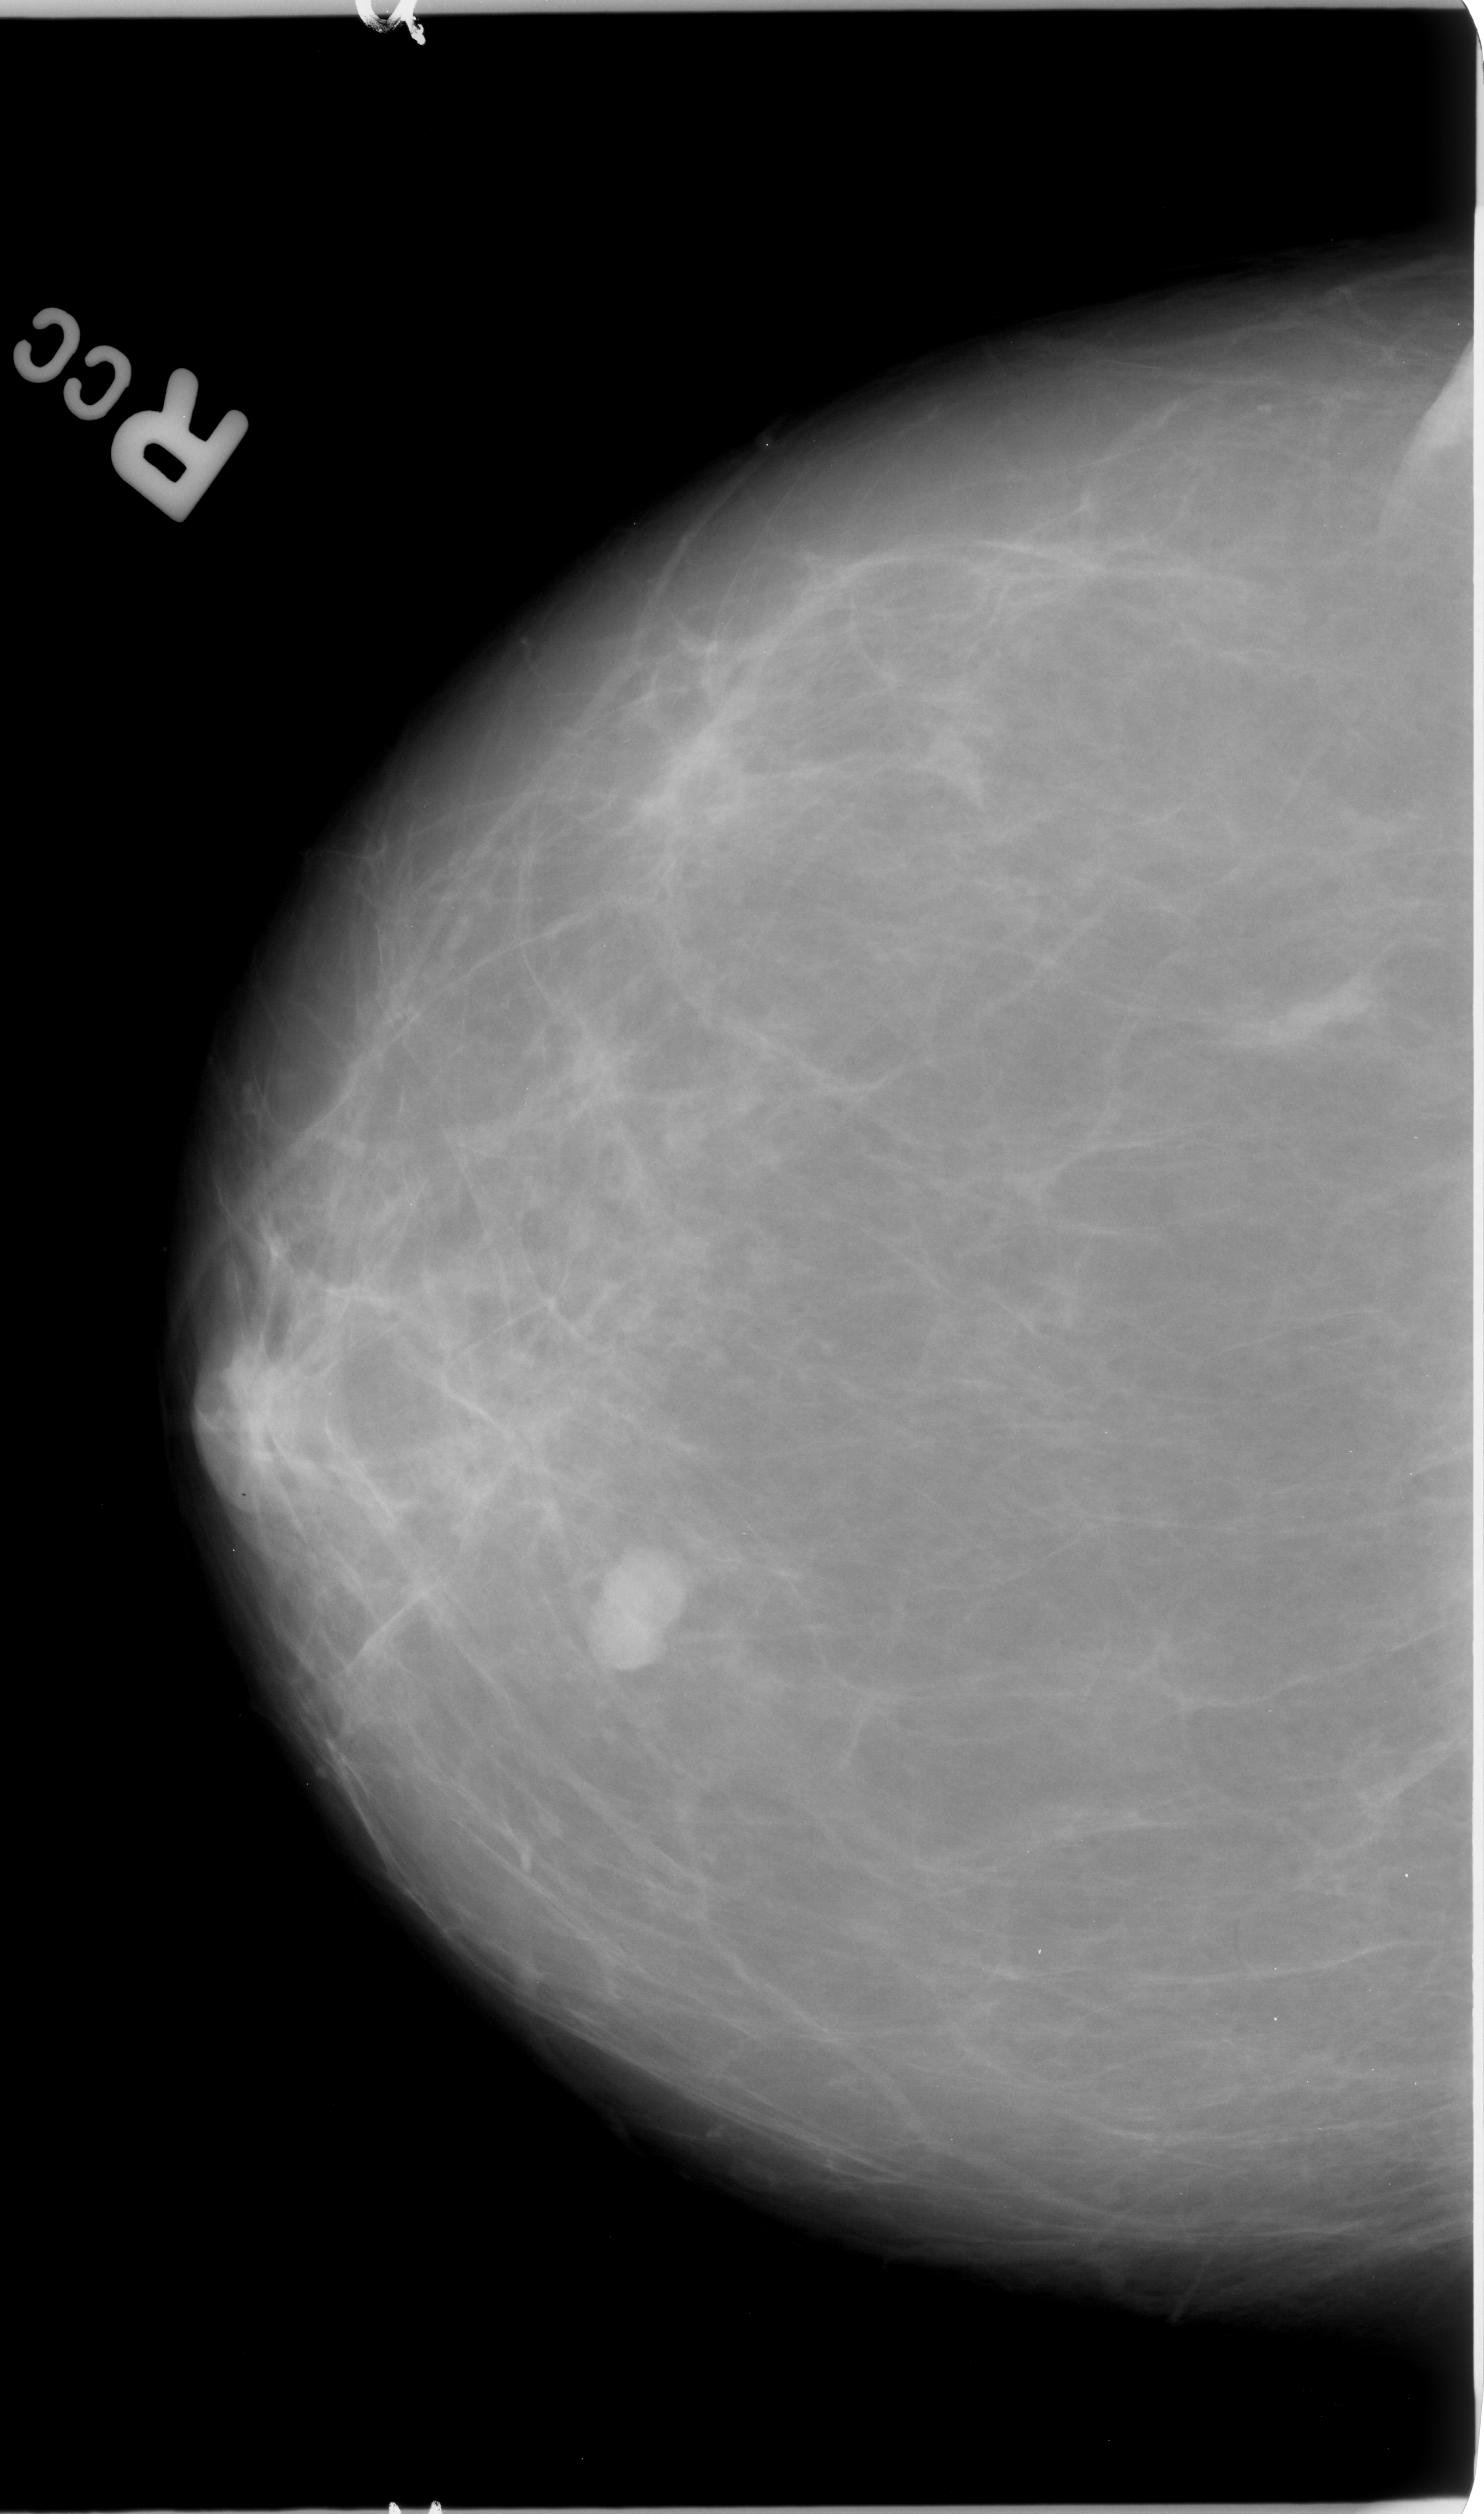
Digitized screen-film mammogram; right breast; CC view; breast composition: almost entirely fatty (BI-RADS density category 1 of 4).
Radiologist-marked abnormalities on this image: mass, shape lobulated, margins circumscribed / ill defined; BI-RADS assessment category 4; subtlety rating 5 on a 1 (subtle) to 5 (obvious) scale; pathology result (as recorded, not read from the image): malignant.